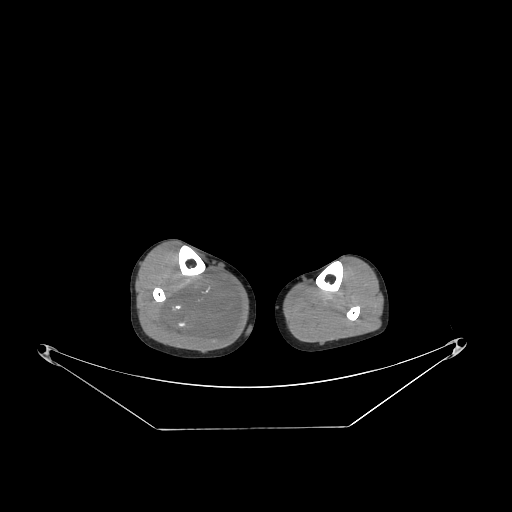
CT of an extremity soft-tissue mass (from a PET/CT study), one axial slice. Position 102 of 267 along the scan axis. Reconstruction kernel STANDARD. Soft-tissue window (W 400 / L 40 HU). 3.75 mm slice thickness. 512 × 512 image matrix, field of view 500 × 500 mm. Male patient. Case-level facts recorded for this patient, not image findings: histological type: liposarcoma - round cell; grade: high; site of the primary tumour: right calf.
Annotated regions visible in this slice (expert contour drawn on MRI and transferred to this co-registered scan by the dataset authors):
- gross tumour volume (mass): bounding box <155,272,241,346> (left, top, right, bottom; pixels)